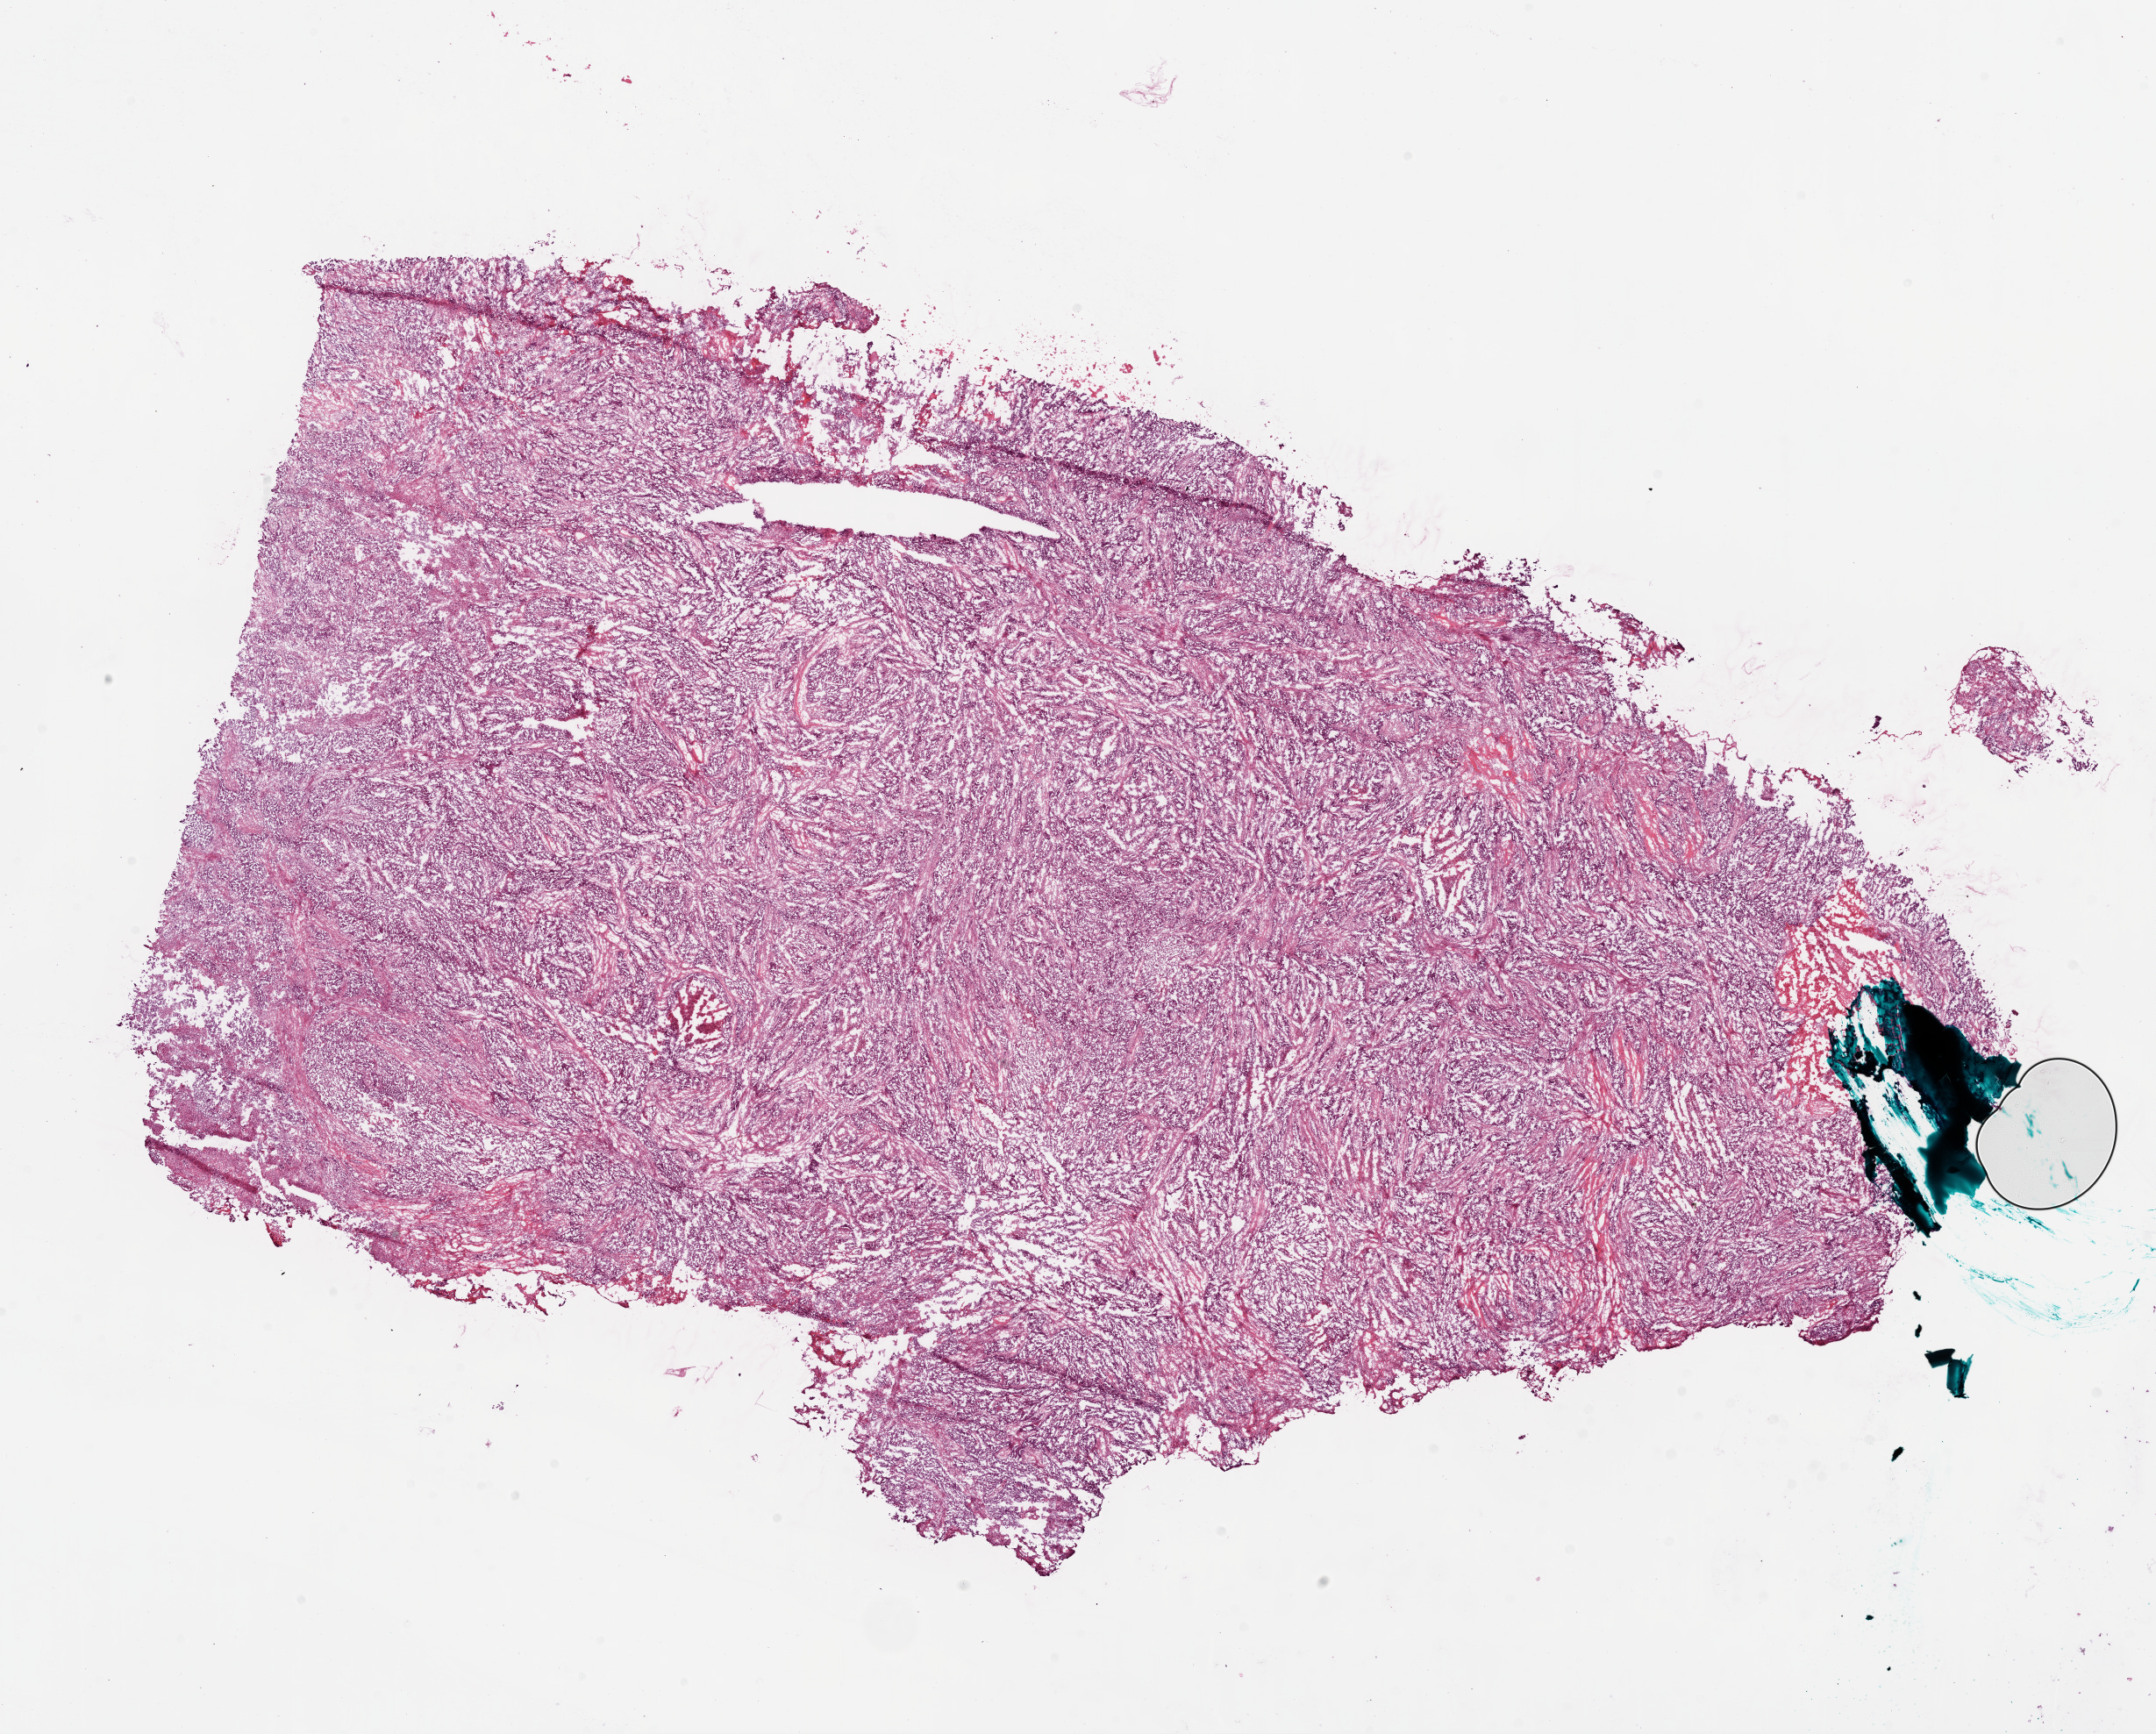
Whole-slide histology image, Hematoxylin and eosin (H&E) stained, shown as a low-resolution overview of the whole scanned area (about 19.8 x 15.9 mm); frozen section from the bottom of the tissue portion; ovary, primary tumour sample. Female, age 55 years at initial diagnosis. Histologic grade: G3 (poorly differentiated). Composition of this section per pathologist review: tumour cells 90%, tumour nuclei 99%, normal cells 0%, stromal cells 1%, necrosis 9%. Inflammatory infiltration, as recorded: lymphocyte infiltration 10%.
• FIGO stage: IV
• diagnosis: Serous cystadenocarcinoma, NOS